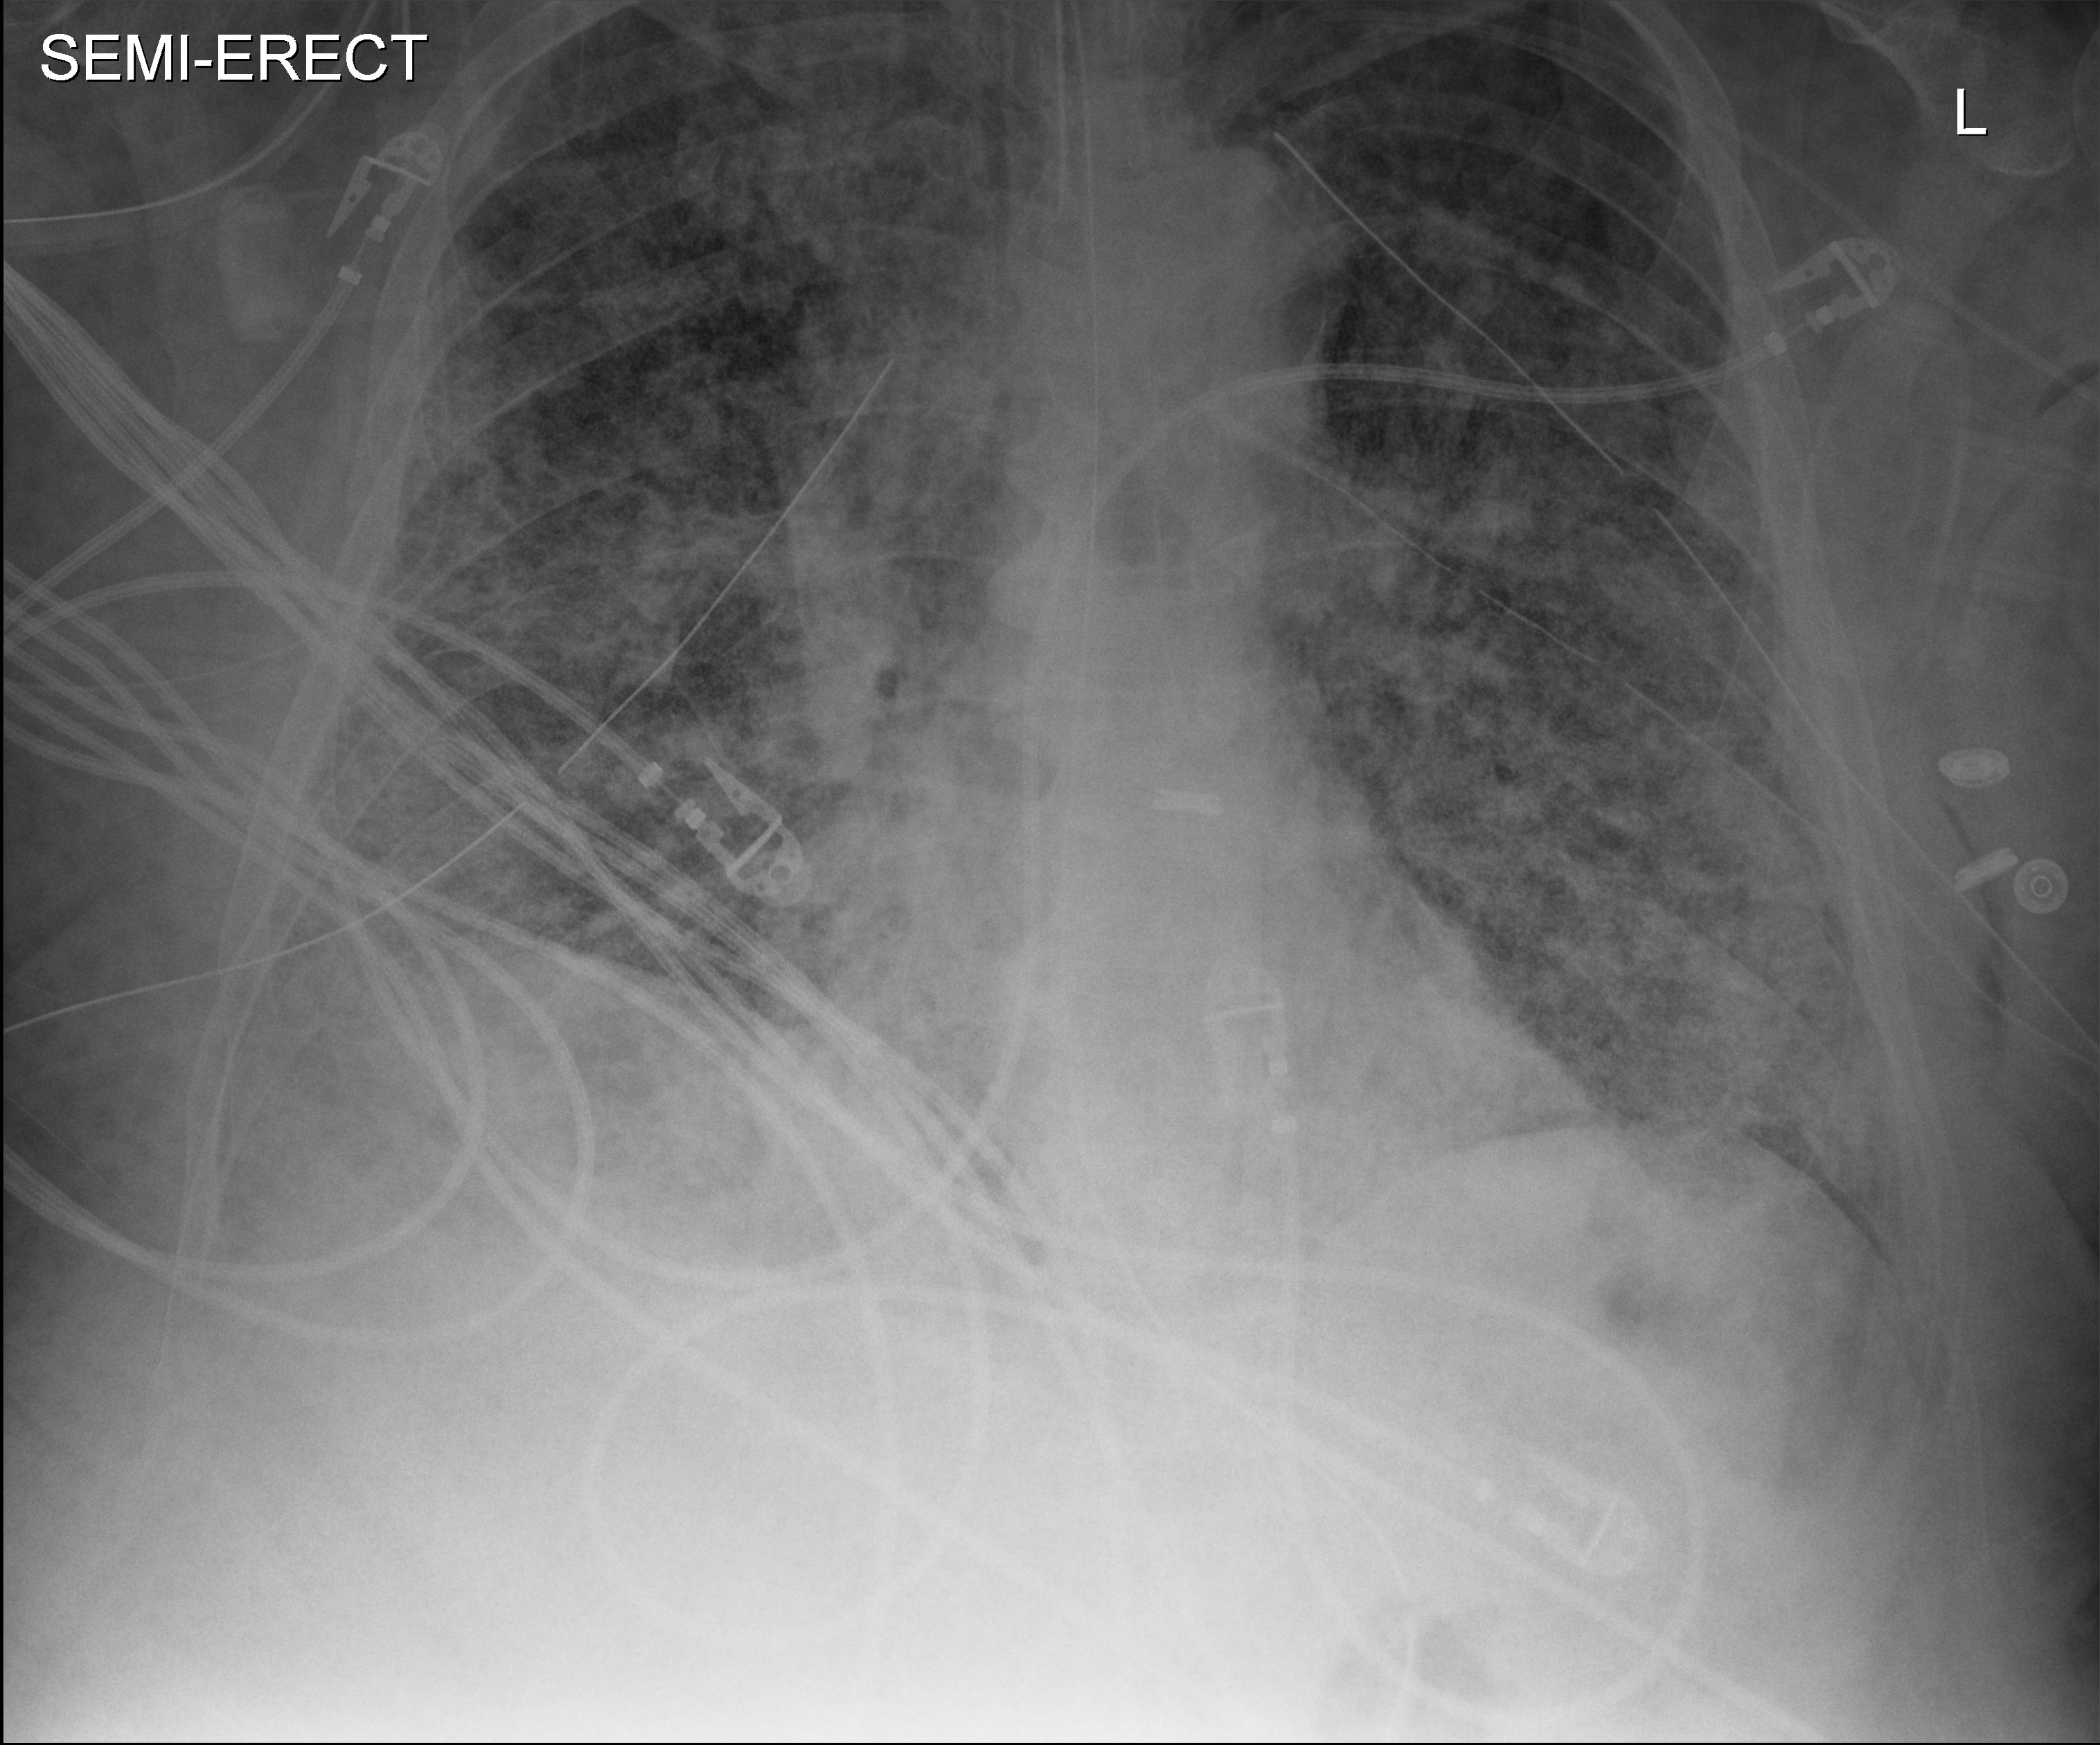
Chest X-ray (portable); anteroposterior (AP) projection. Adult patient hospitalised with COVID-19, age 18–59 years.
Hospital-stay facts (about this admission, not read from this image; timing relative to this image not recorded):
- admitted to intensive care during this hospital stay: yes